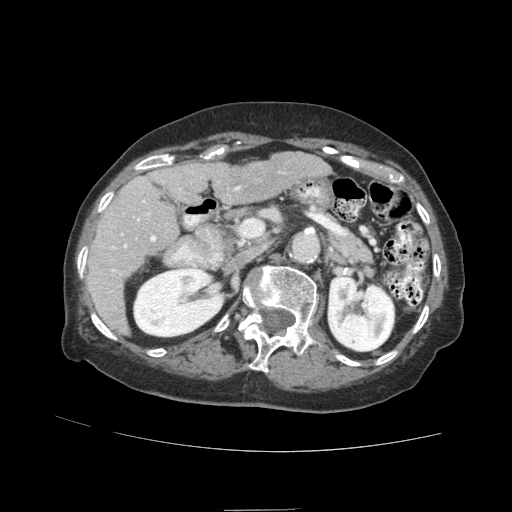
Contrast-enhanced abdominal CT (liver protocol), one axial slice; position 45 of 89 along the scan axis; reconstruction kernel STANDARD; 140 kVp; soft-tissue window (W 400 / L 40 HU); 512 × 512 image matrix, field of view 360 × 360 mm. Case-level facts recorded for this patient, not image findings: diagnosis: hepatocellular carcinoma (patient treated with transarterial chemoembolisation; whether this scan precedes or follows treatment is not stated here); TNM stage (as recorded): Stage-II.
Outlined on this slice (semi-automatically segmented with operator editing):
- liver parenchyma outside the tumour (the mass and vessels are separate outlines, so this box may not span the whole liver): box from (x=86, y=152) to (x=330, y=334) px
- mass: (x=242, y=163)–(x=272, y=187)
- liver vessels: (x=110, y=172)–(x=284, y=309)